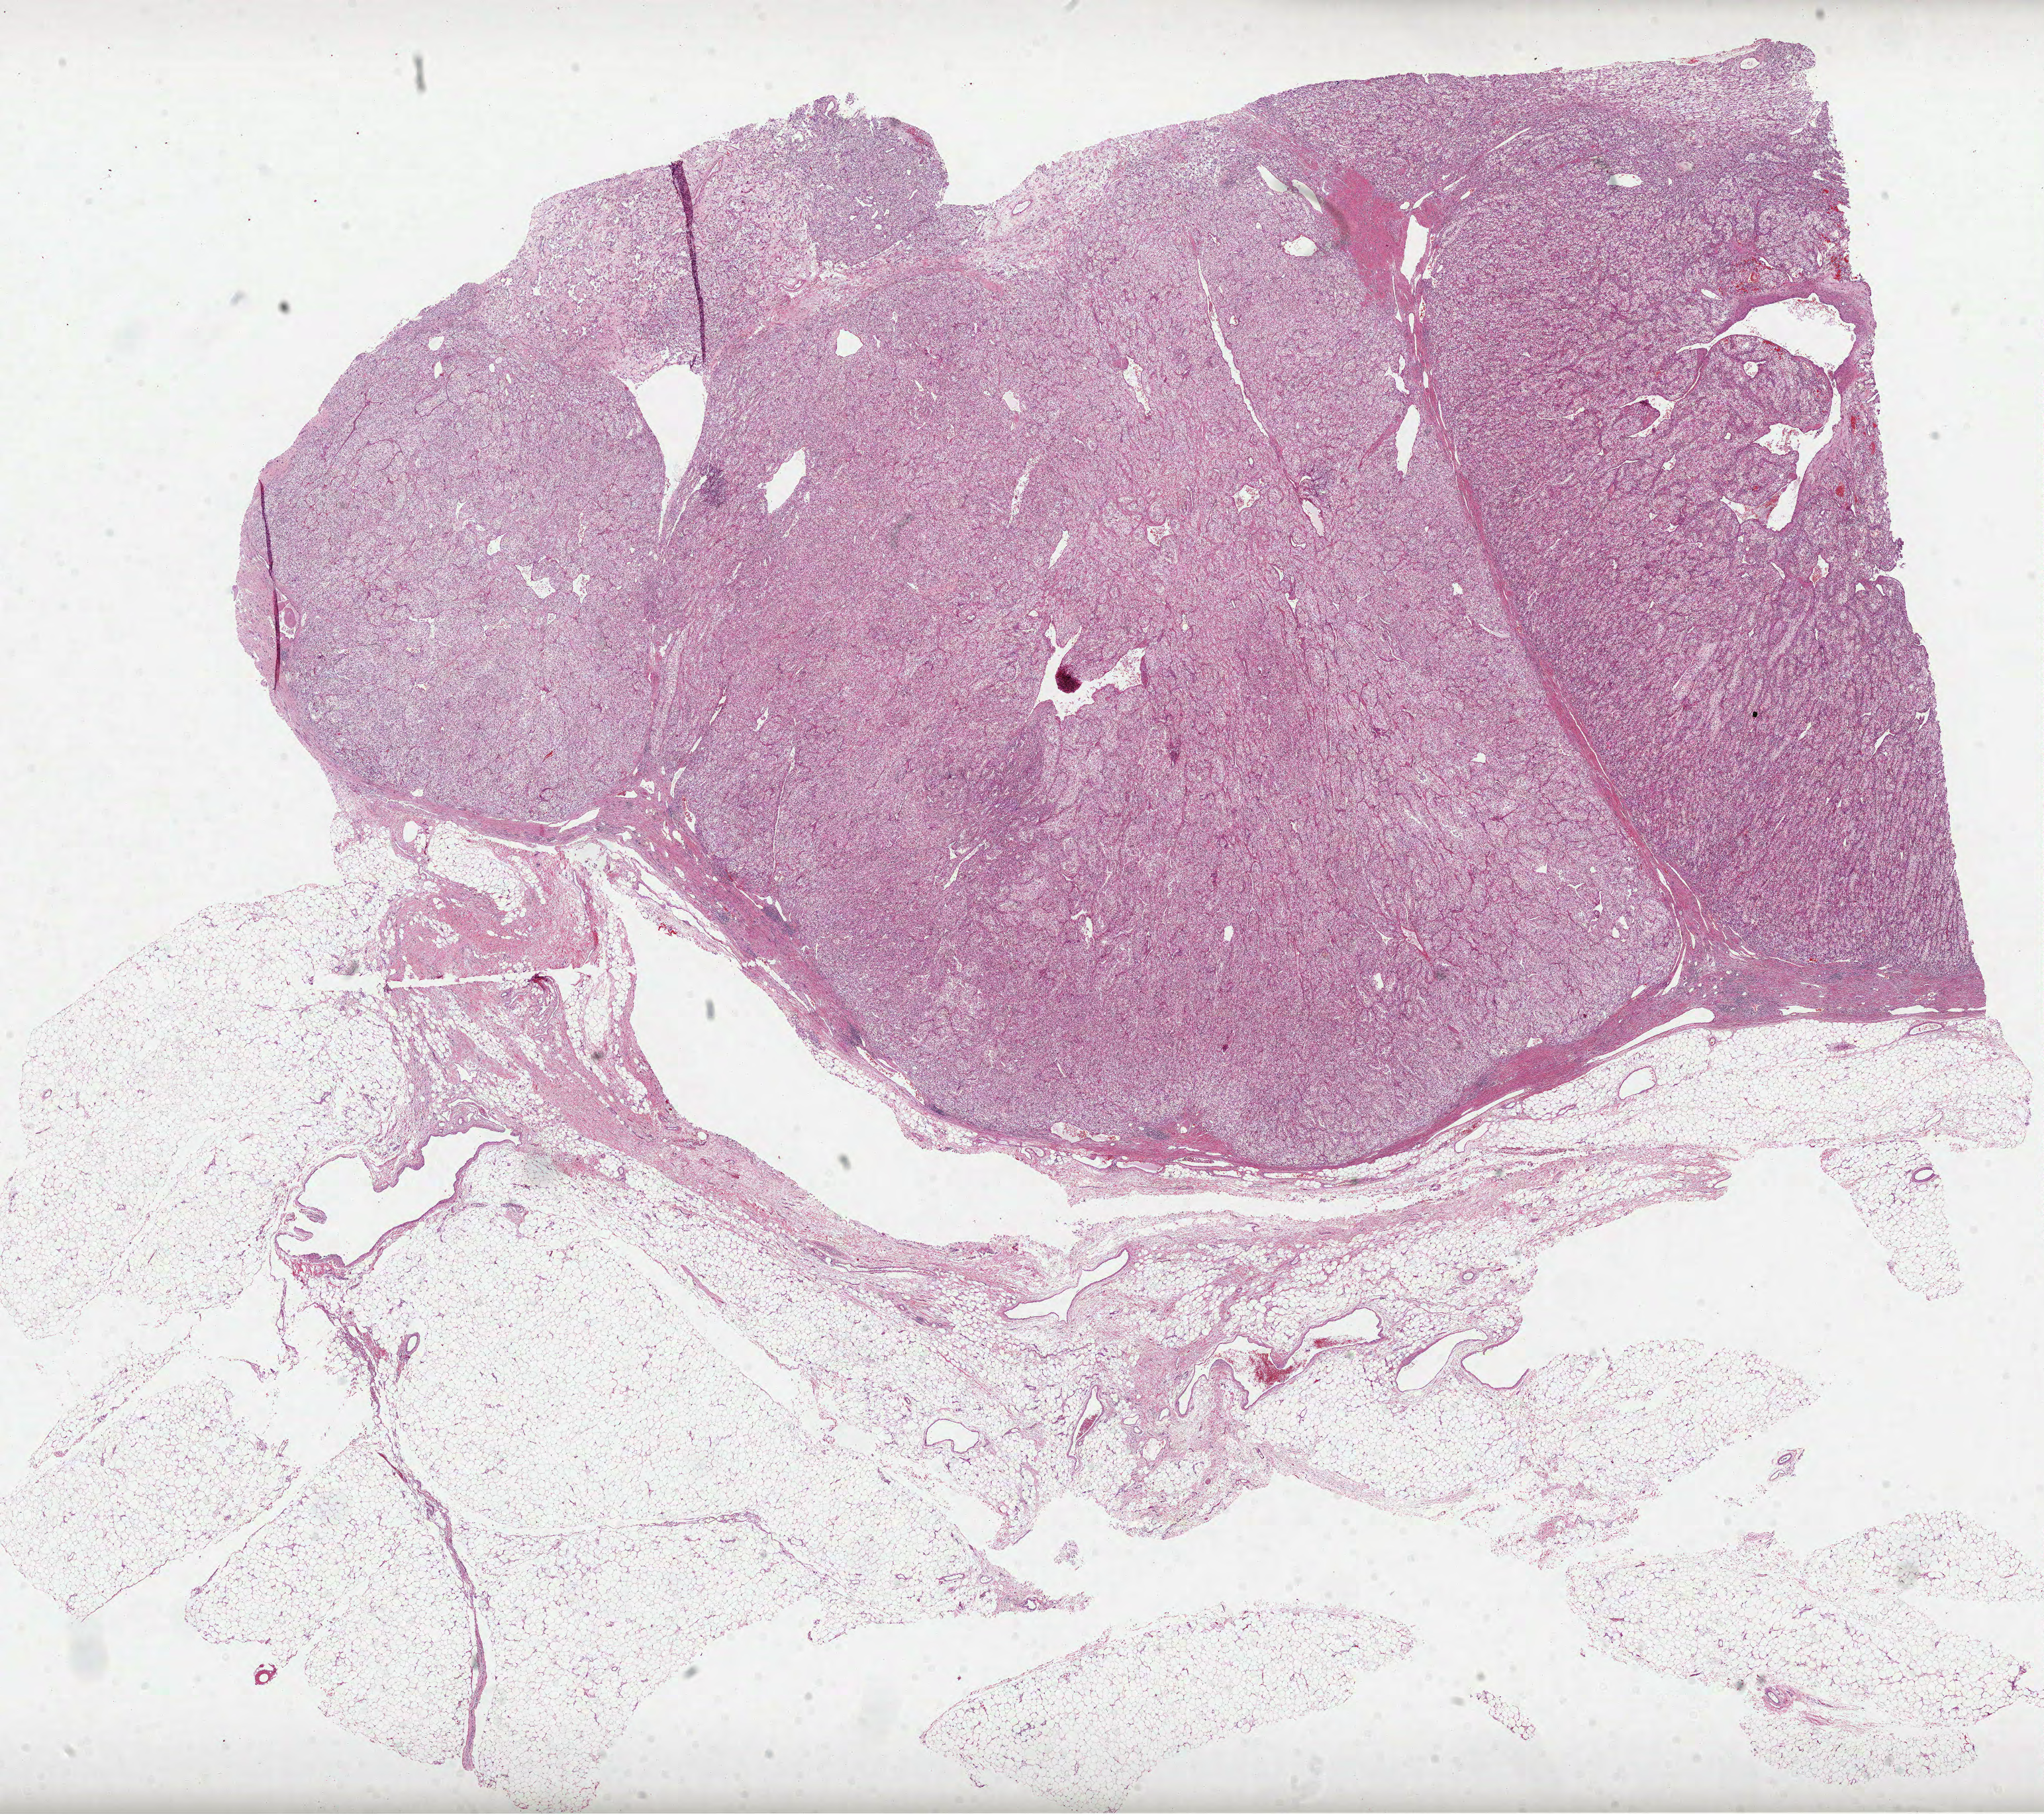
Digitized H&E-stained tissue section (whole slide) — a low-resolution overview of the entire scanned area, about 24.9 x 22.1 mm. Formalin-fixed paraffin-embedded (FFPE) diagnostic section. Kidney, primary tumour sample. Male, age 63 years at initial diagnosis. Histologic grade: G3 (poorly differentiated).
AJCC pathologic stage: IV. TNM: T2 NX M1. Histologic diagnosis: Clear cell adenocarcinoma, NOS.